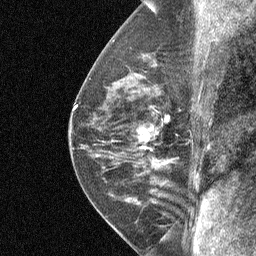
Breast MRI (dynamic contrast-enhanced), one sagittal slice; position 39 of 64 along the scan axis; dynamic contrast-enhanced study with each time point stored as its own series, time point 2 of 4 at this slice position (early post-contrast, ordered by acquisition time); 1.5 T; TE 4.8 ms, TR 27 ms; 256 × 256 image matrix, field of view 180 × 180 mm. Female patient, age 50 years. From the clinical record (not read from this slice): setting: breast cancer imaged before/during neoadjuvant chemotherapy; receptor status: HER2-positive.
Structures marked on this image (semi-automatic segmentation, software-assisted and operator-edited):
- analysis volume of interest (the breast-tissue region the enhancement analysis was run in; not a lesion): box from (x=123, y=91) to (x=180, y=177) px
- tumour enhancement mask (voxels above the 90 % enhancement threshold inside the analysis volume of interest): (x=138, y=128)–(x=153, y=141)